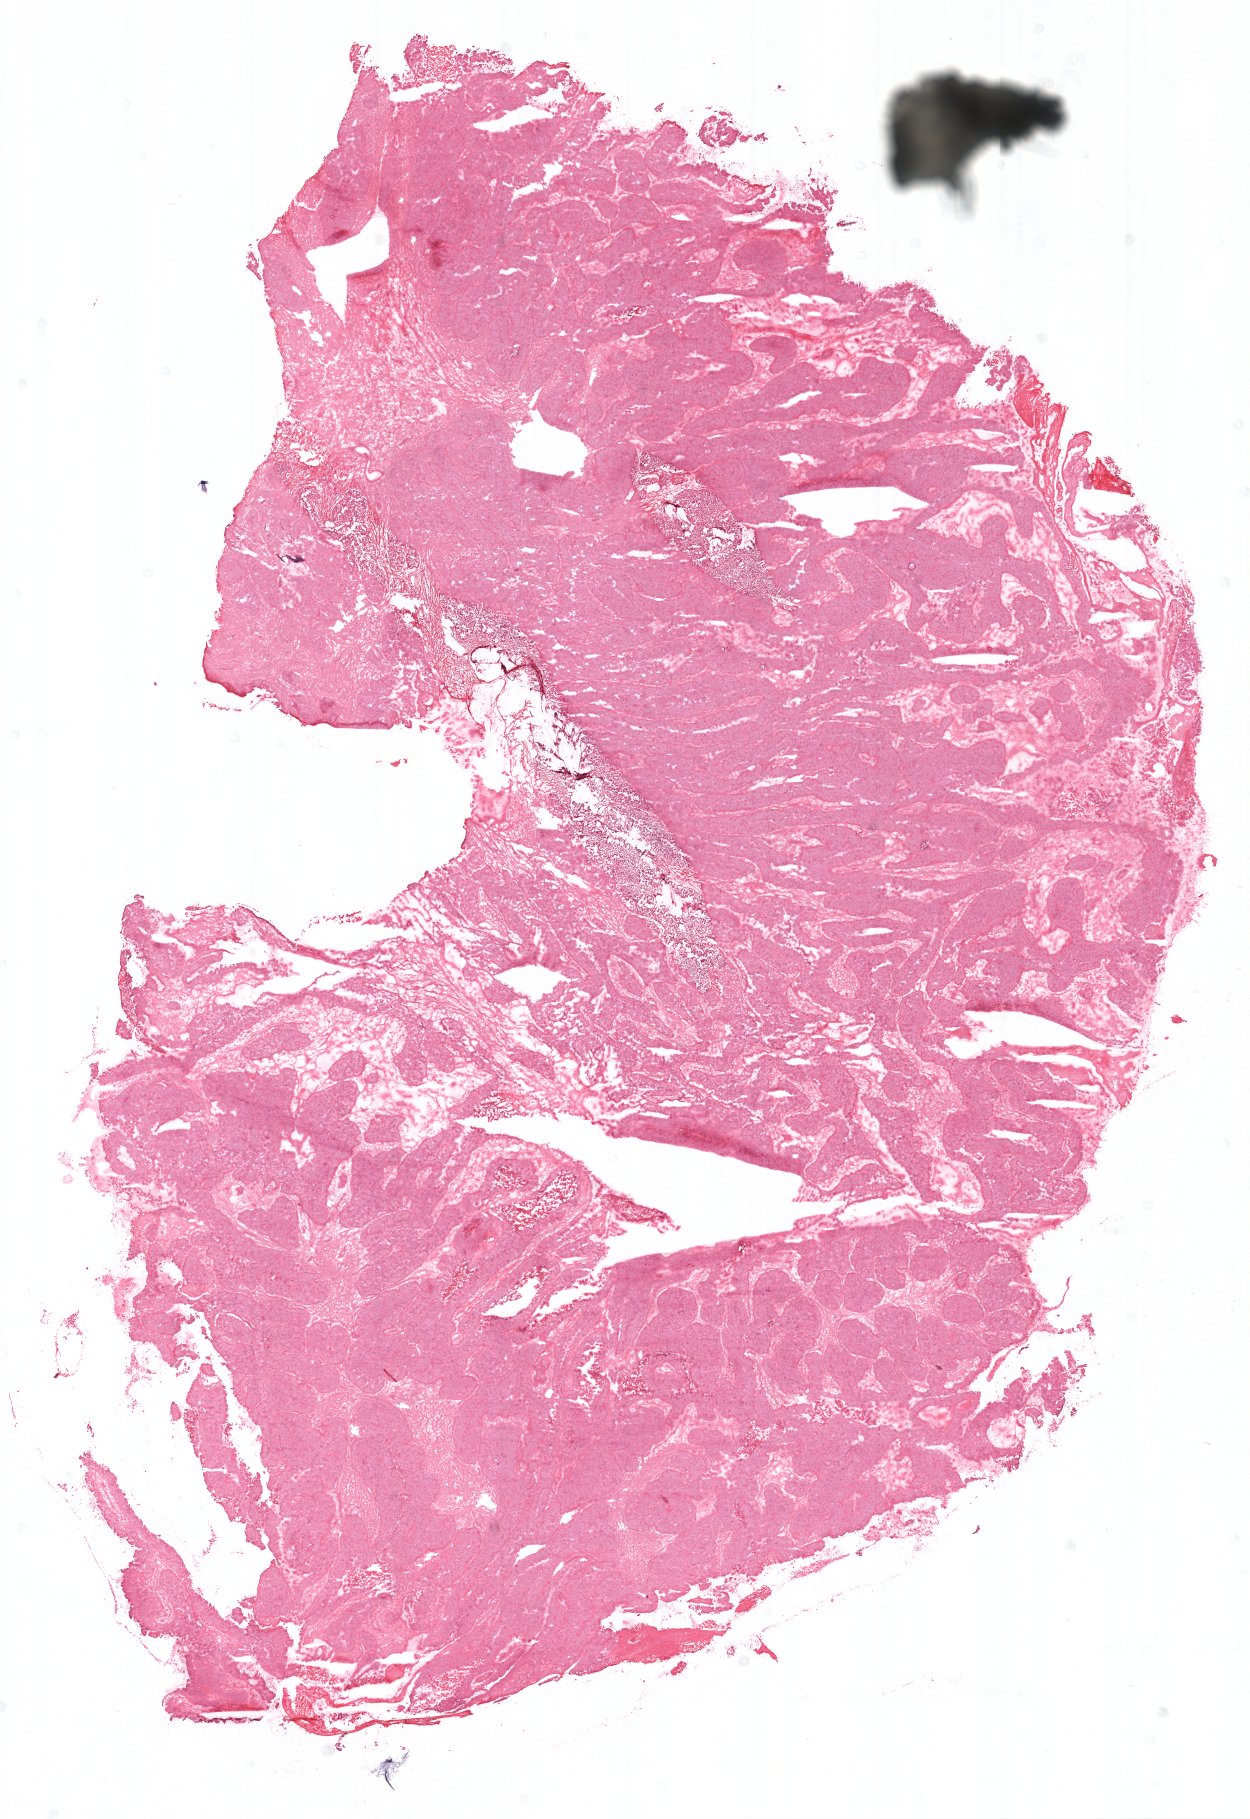
Digitized Hematoxylin and eosin (H&E) stained tissue section (whole slide) — low-resolution overview of the scanned area, about 10.0 x 14.6 mm, frozen section from the top of the tissue portion, sample: primary tumour, ovary. Patient: female, age at initial diagnosis 78 years. Histologic grade: G3 (poorly differentiated). Pathologist review of this section (percent, as recorded): tumour cells 85%, tumour nuclei 90%, normal cells 0%, stromal cells 0%, necrosis 15%.
Diagnosis: Serous cystadenocarcinoma, NOS. FIGO stage: IC.